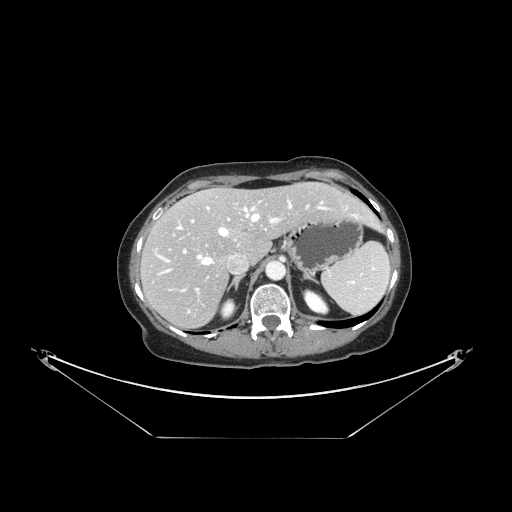
Contrast-enhanced abdominal CT, one axial slice; slice 106 of 148 in the series (ordered by position); reconstruction kernel STANDARD; 120 kVp; intravenous contrast given; soft-tissue window (W 400 / L 40 HU); 2.5 mm slice thickness; 512 × 512 image matrix, field of view 500 × 500 mm. Female patient, age 73 years. From the clinical record (not read from this slice): diagnosis: colorectal cancer liver metastases, imaged before liver resection; multiple liver metastases: no; largest metastasis: 1 cm; chemotherapy before resection: yes.
Structures marked on this image (outlined manually by an expert reader):
- hepatic veins: box from (x=162, y=200) to (x=359, y=272) px
- liver: (x=143, y=184)–(x=378, y=328)
- planned liver remnant (the part of the liver to remain after resection): (x=168, y=183)–(x=376, y=260)
- portal vein (with intrahepatic branches): (x=181, y=206)–(x=308, y=292)